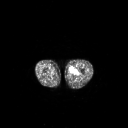
FDG PET of an extremity soft-tissue mass (from a PET/CT study), one axial slice. Position 225 of 267 along the scan axis. 3.27 mm slice thickness. 128 × 128 image matrix, field of view 700 × 700 mm. Male patient, age 63 years. From the clinical record (not read from this slice): histological type: pleiomorphic liposarcoma; grade: high; site of the primary tumour: left thigh.
Outlined on this slice (expert contour drawn on MRI and transferred to this co-registered scan by the dataset authors):
- gross tumour volume including surrounding oedema: bounding box (x1, y1, x2, y2) in pixels: (70, 66, 79, 75)
- gross tumour volume (mass): (70, 66, 74, 72)